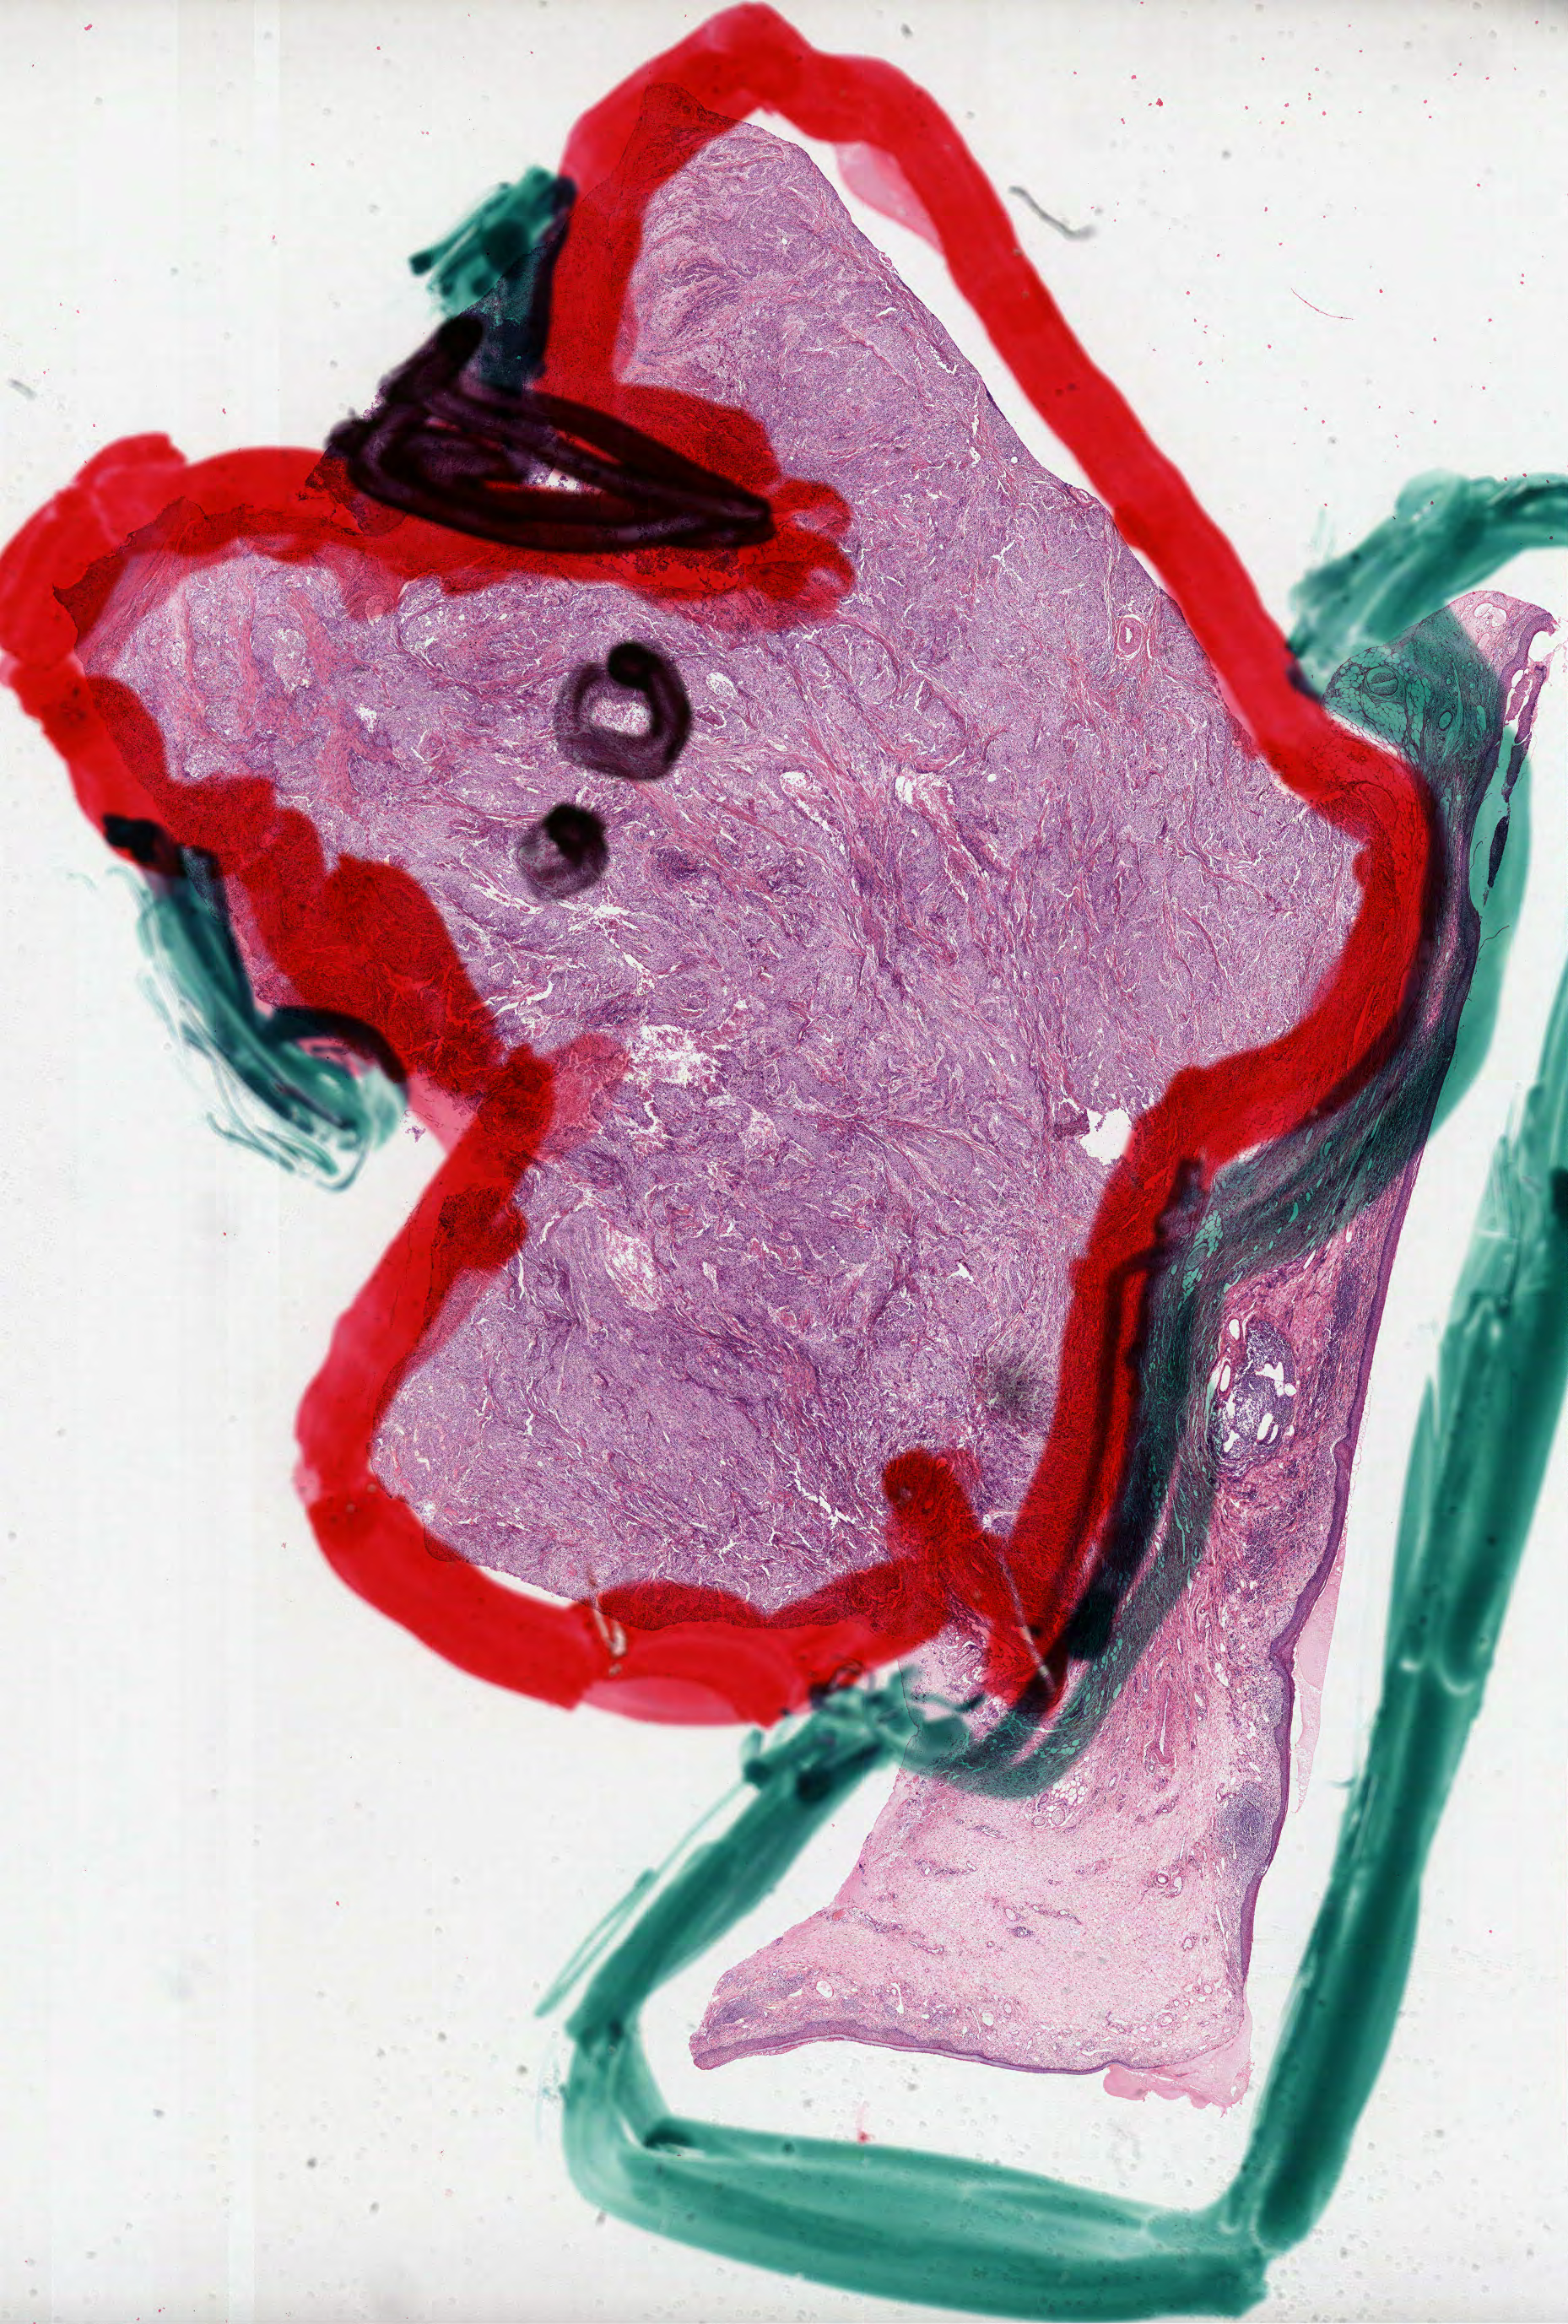
Digitized H&E tissue section (whole slide), a low-resolution overview of the entire scanned area, about 15.0 x 22.2 mm, formalin-fixed paraffin-embedded (FFPE) diagnostic section, head and neck, primary tumour sample. Male, age 58 years at initial diagnosis. Histologic grade: G1 (well differentiated).
AJCC pathologic stage: I (7th edition). Lymph nodes positive (case pathology): 0 of 14 examined. Histologic diagnosis: Squamous cell carcinoma, NOS (larynx, NOS). TNM: T1 N0 M0. Laterality: midline.